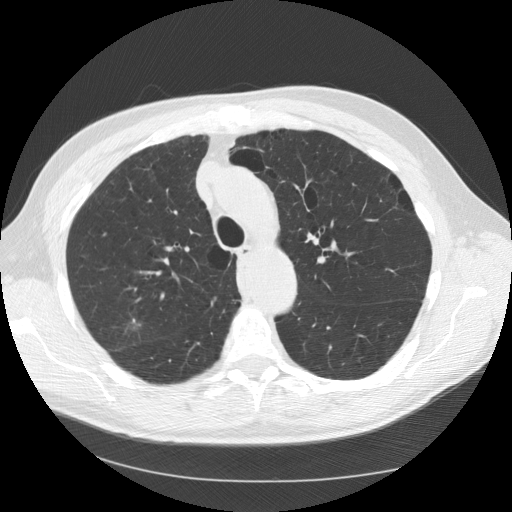
Low-dose screening chest CT, one axial slice; position 94 of 133 along the scan axis; reconstruction kernel STANDARD; 120 kVp; lung window (W 1500 / L -600 HU); 2.5 mm slice thickness; 512 × 512 image matrix.
Outlined on this slice (expert manual segmentation):
- lesion 1 (tumor, upper lobe of right lung): bounding box (x1, y1, x2, y2) in pixels: (132, 318, 141, 326)